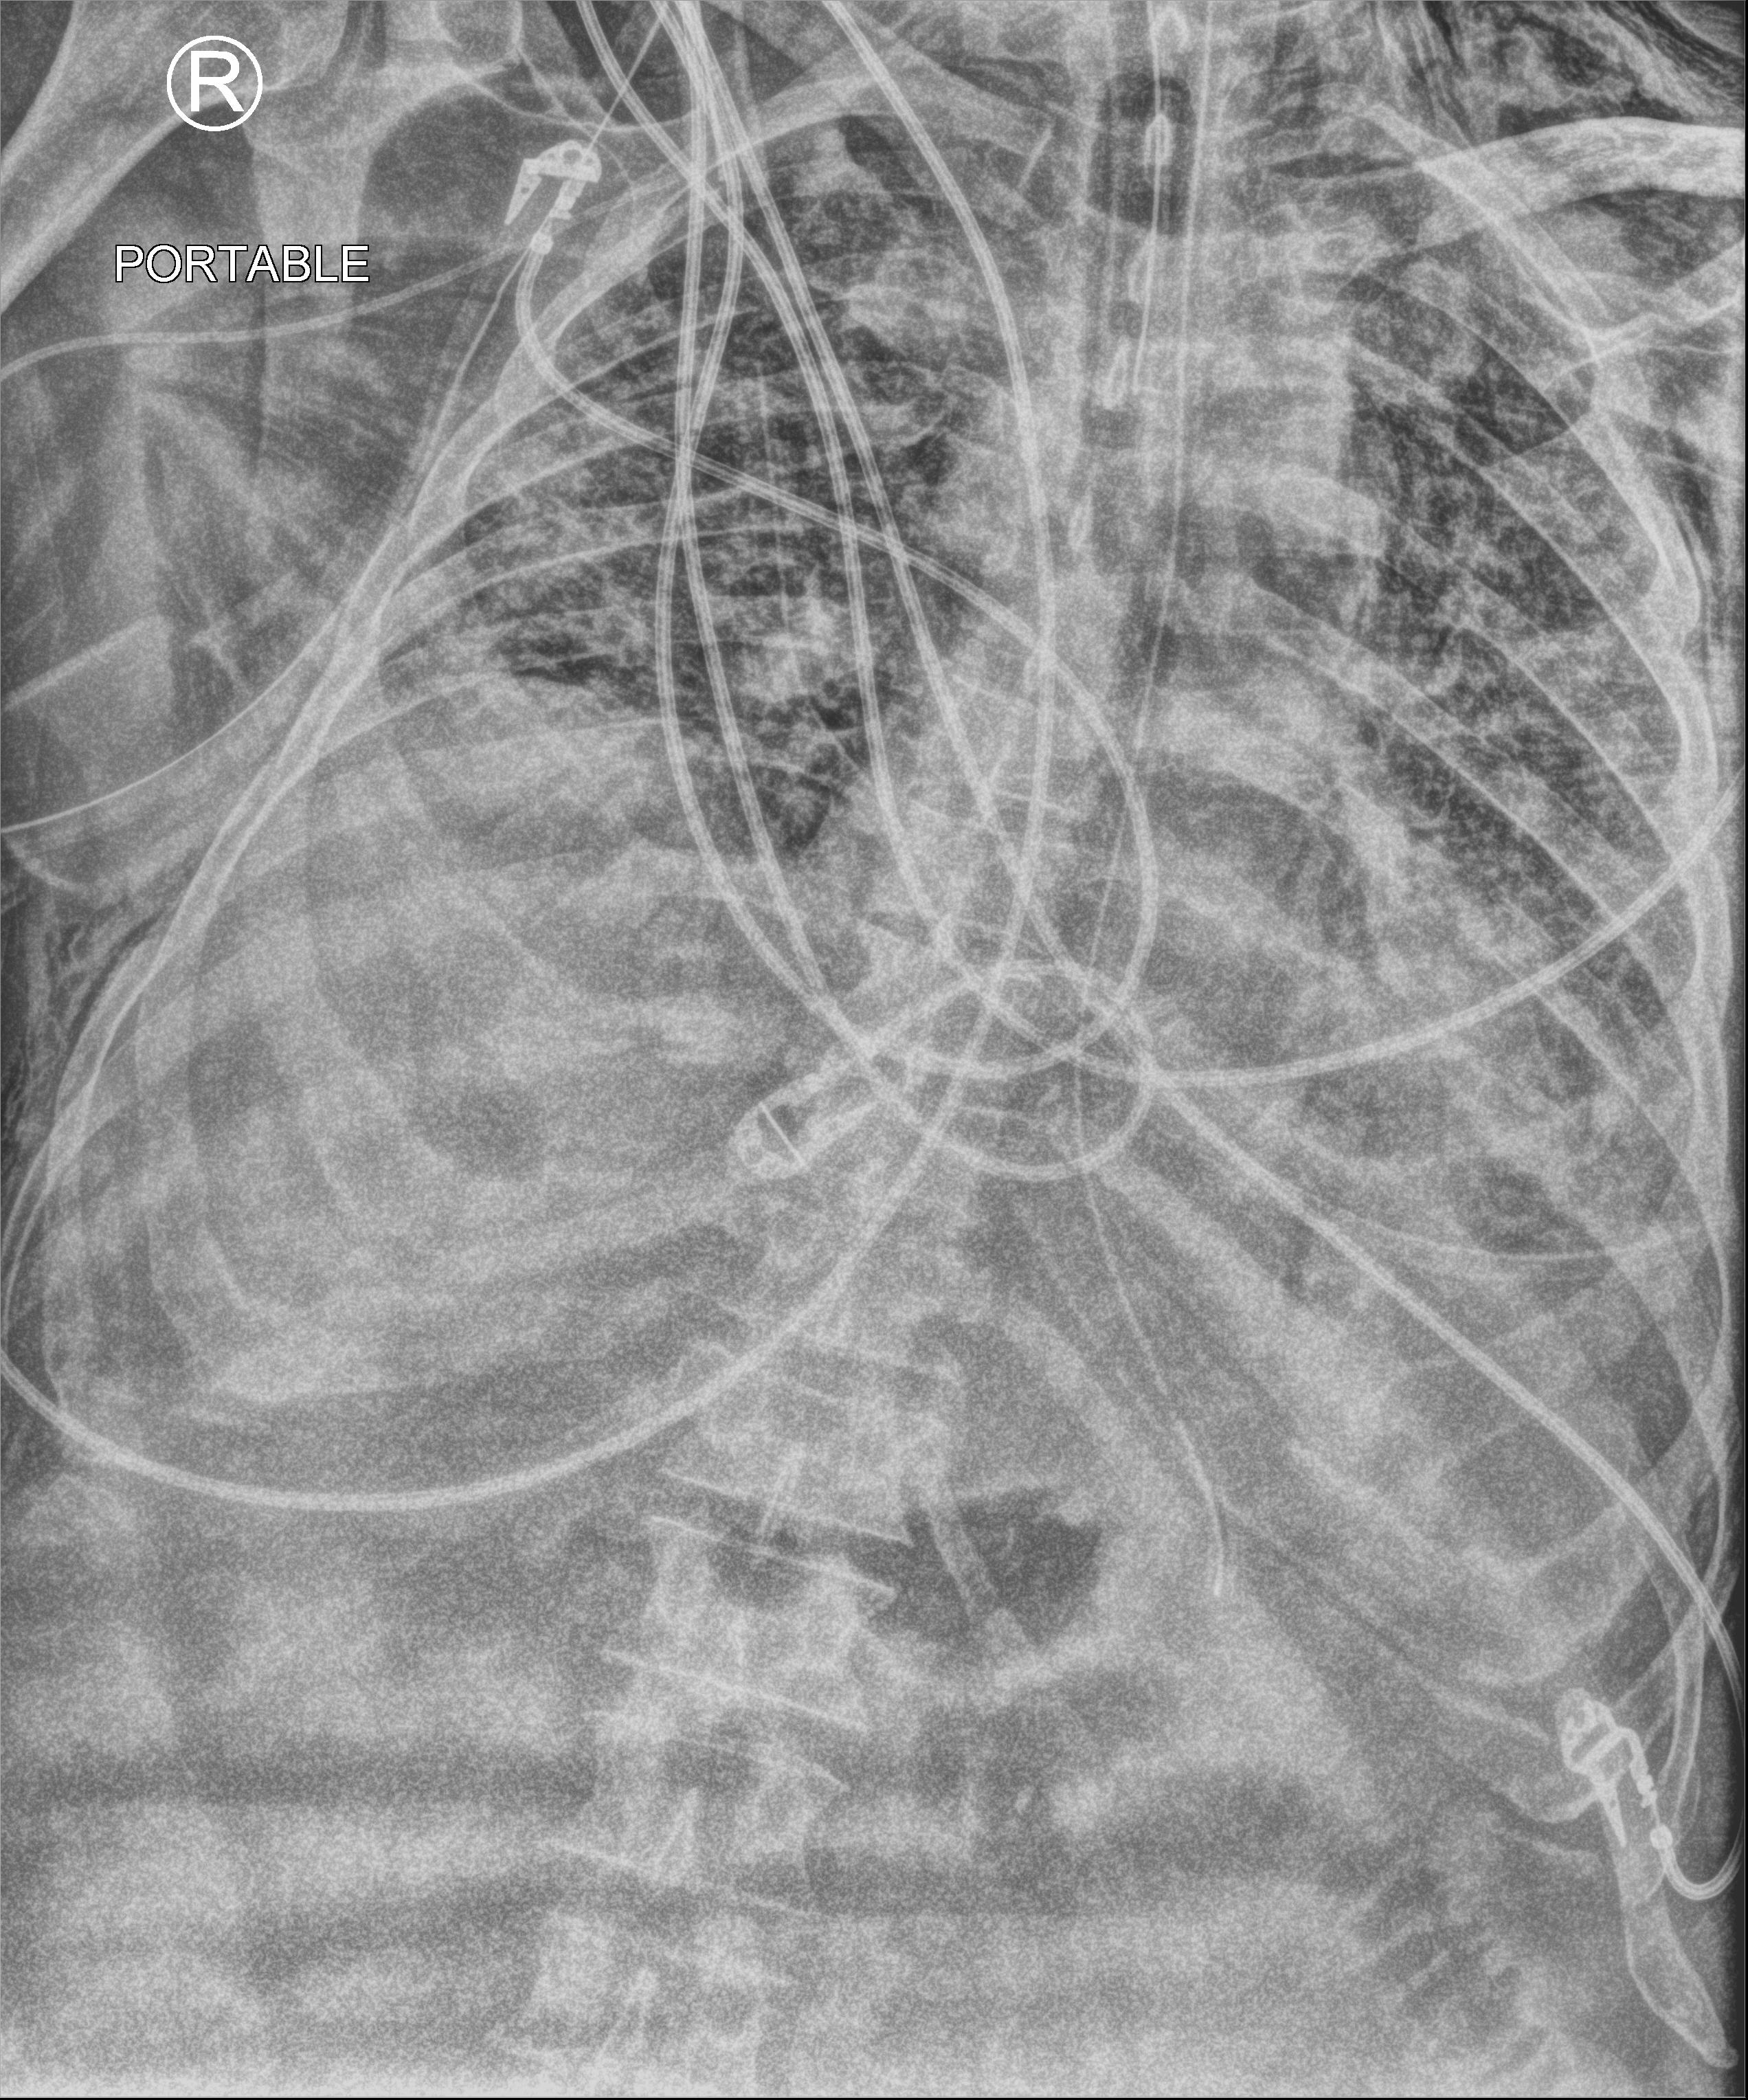
Bedside chest radiograph (computed radiography); anteroposterior (AP) projection. Patient hospitalised with COVID-19; male, aged 60–74 years.
Hospital-stay facts (about this admission, not read from this image; timing relative to this image not recorded):
- admitted to intensive care during this hospital stay: yes
- mechanically ventilated during this hospital stay: yes